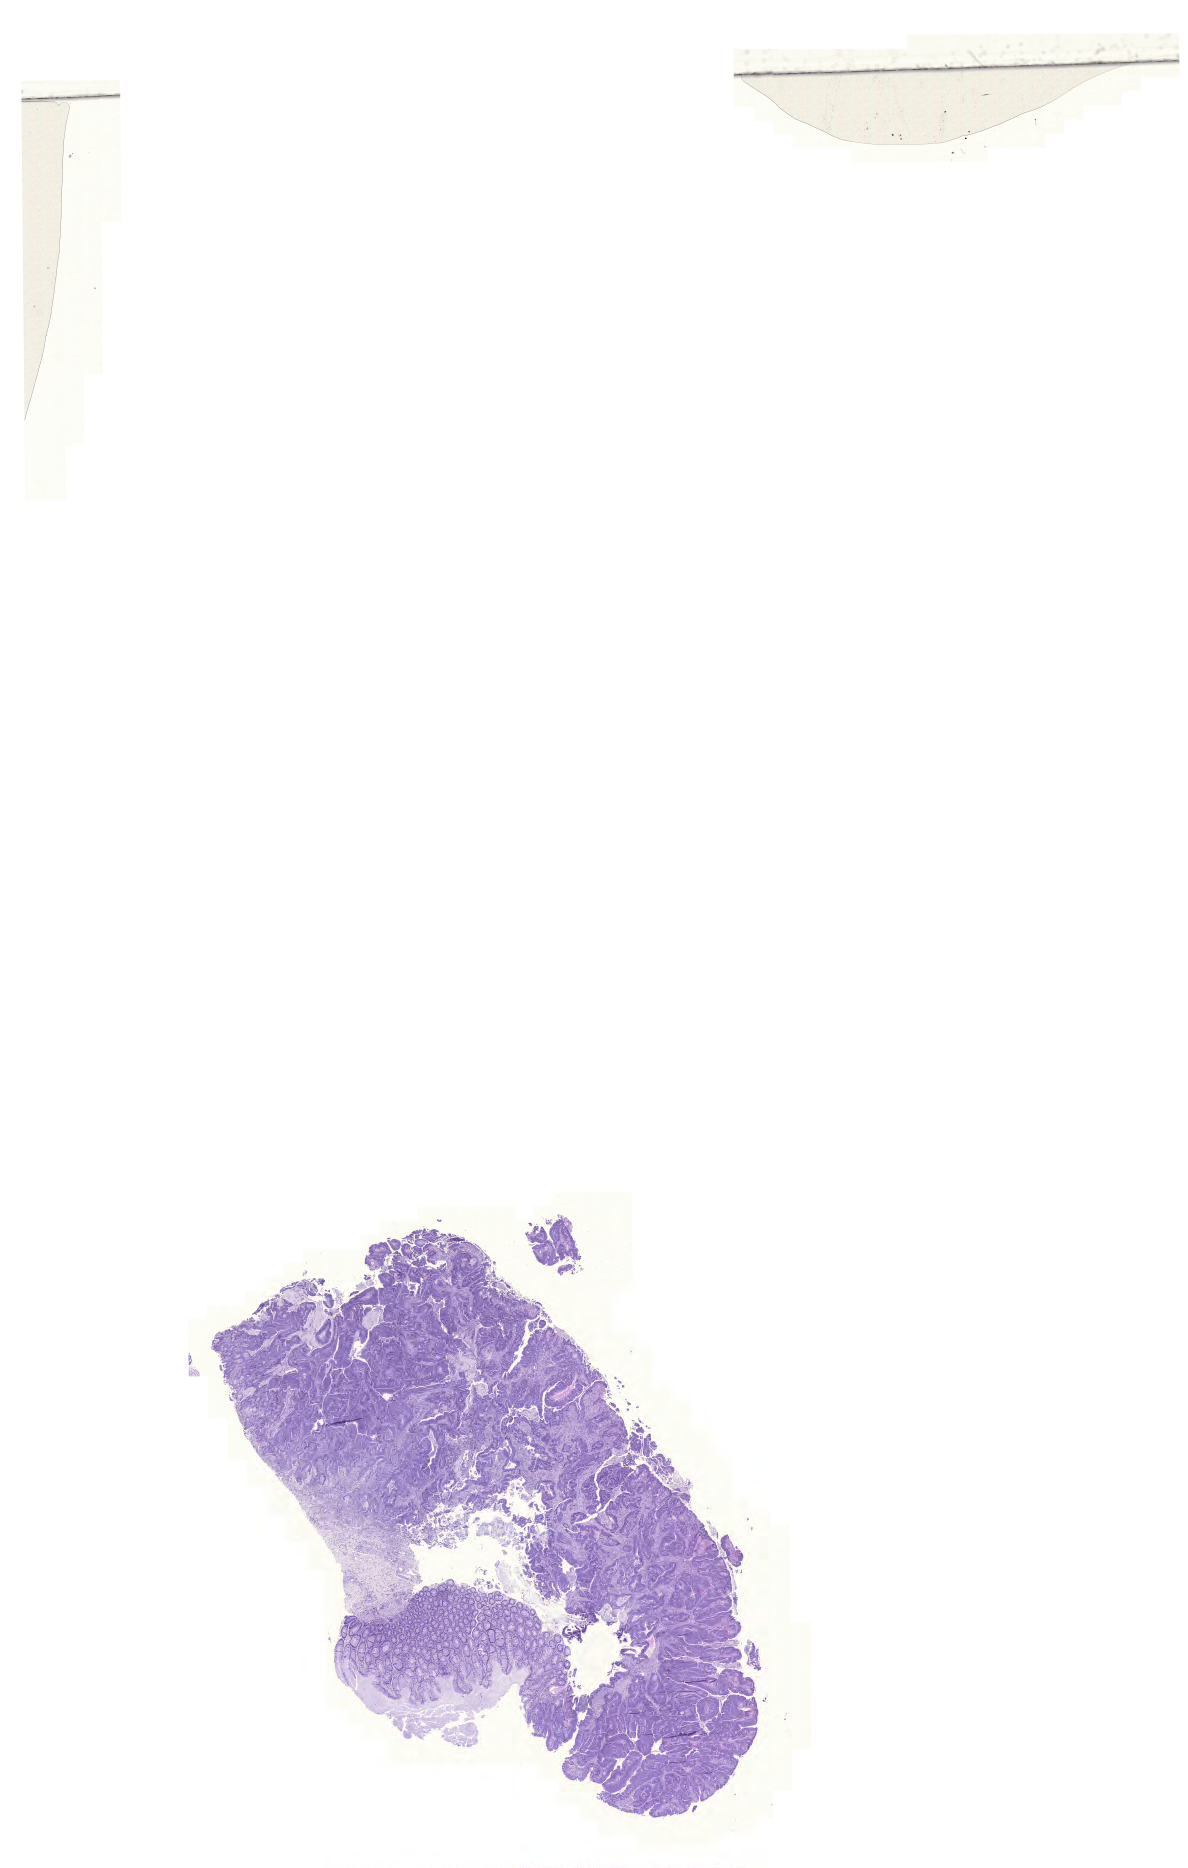
Digitized H&E tissue section (whole slide), low-resolution overview of the scanned area, about 17.7 x 27.8 mm. Formalin-fixed paraffin-embedded (FFPE) diagnostic section. Primary tumour sample from the colon. Male, age 57 years at initial diagnosis.
AJCC pathologic stage: I (6th edition). Histologic diagnosis: Adenocarcinoma, NOS (sigmoid colon).